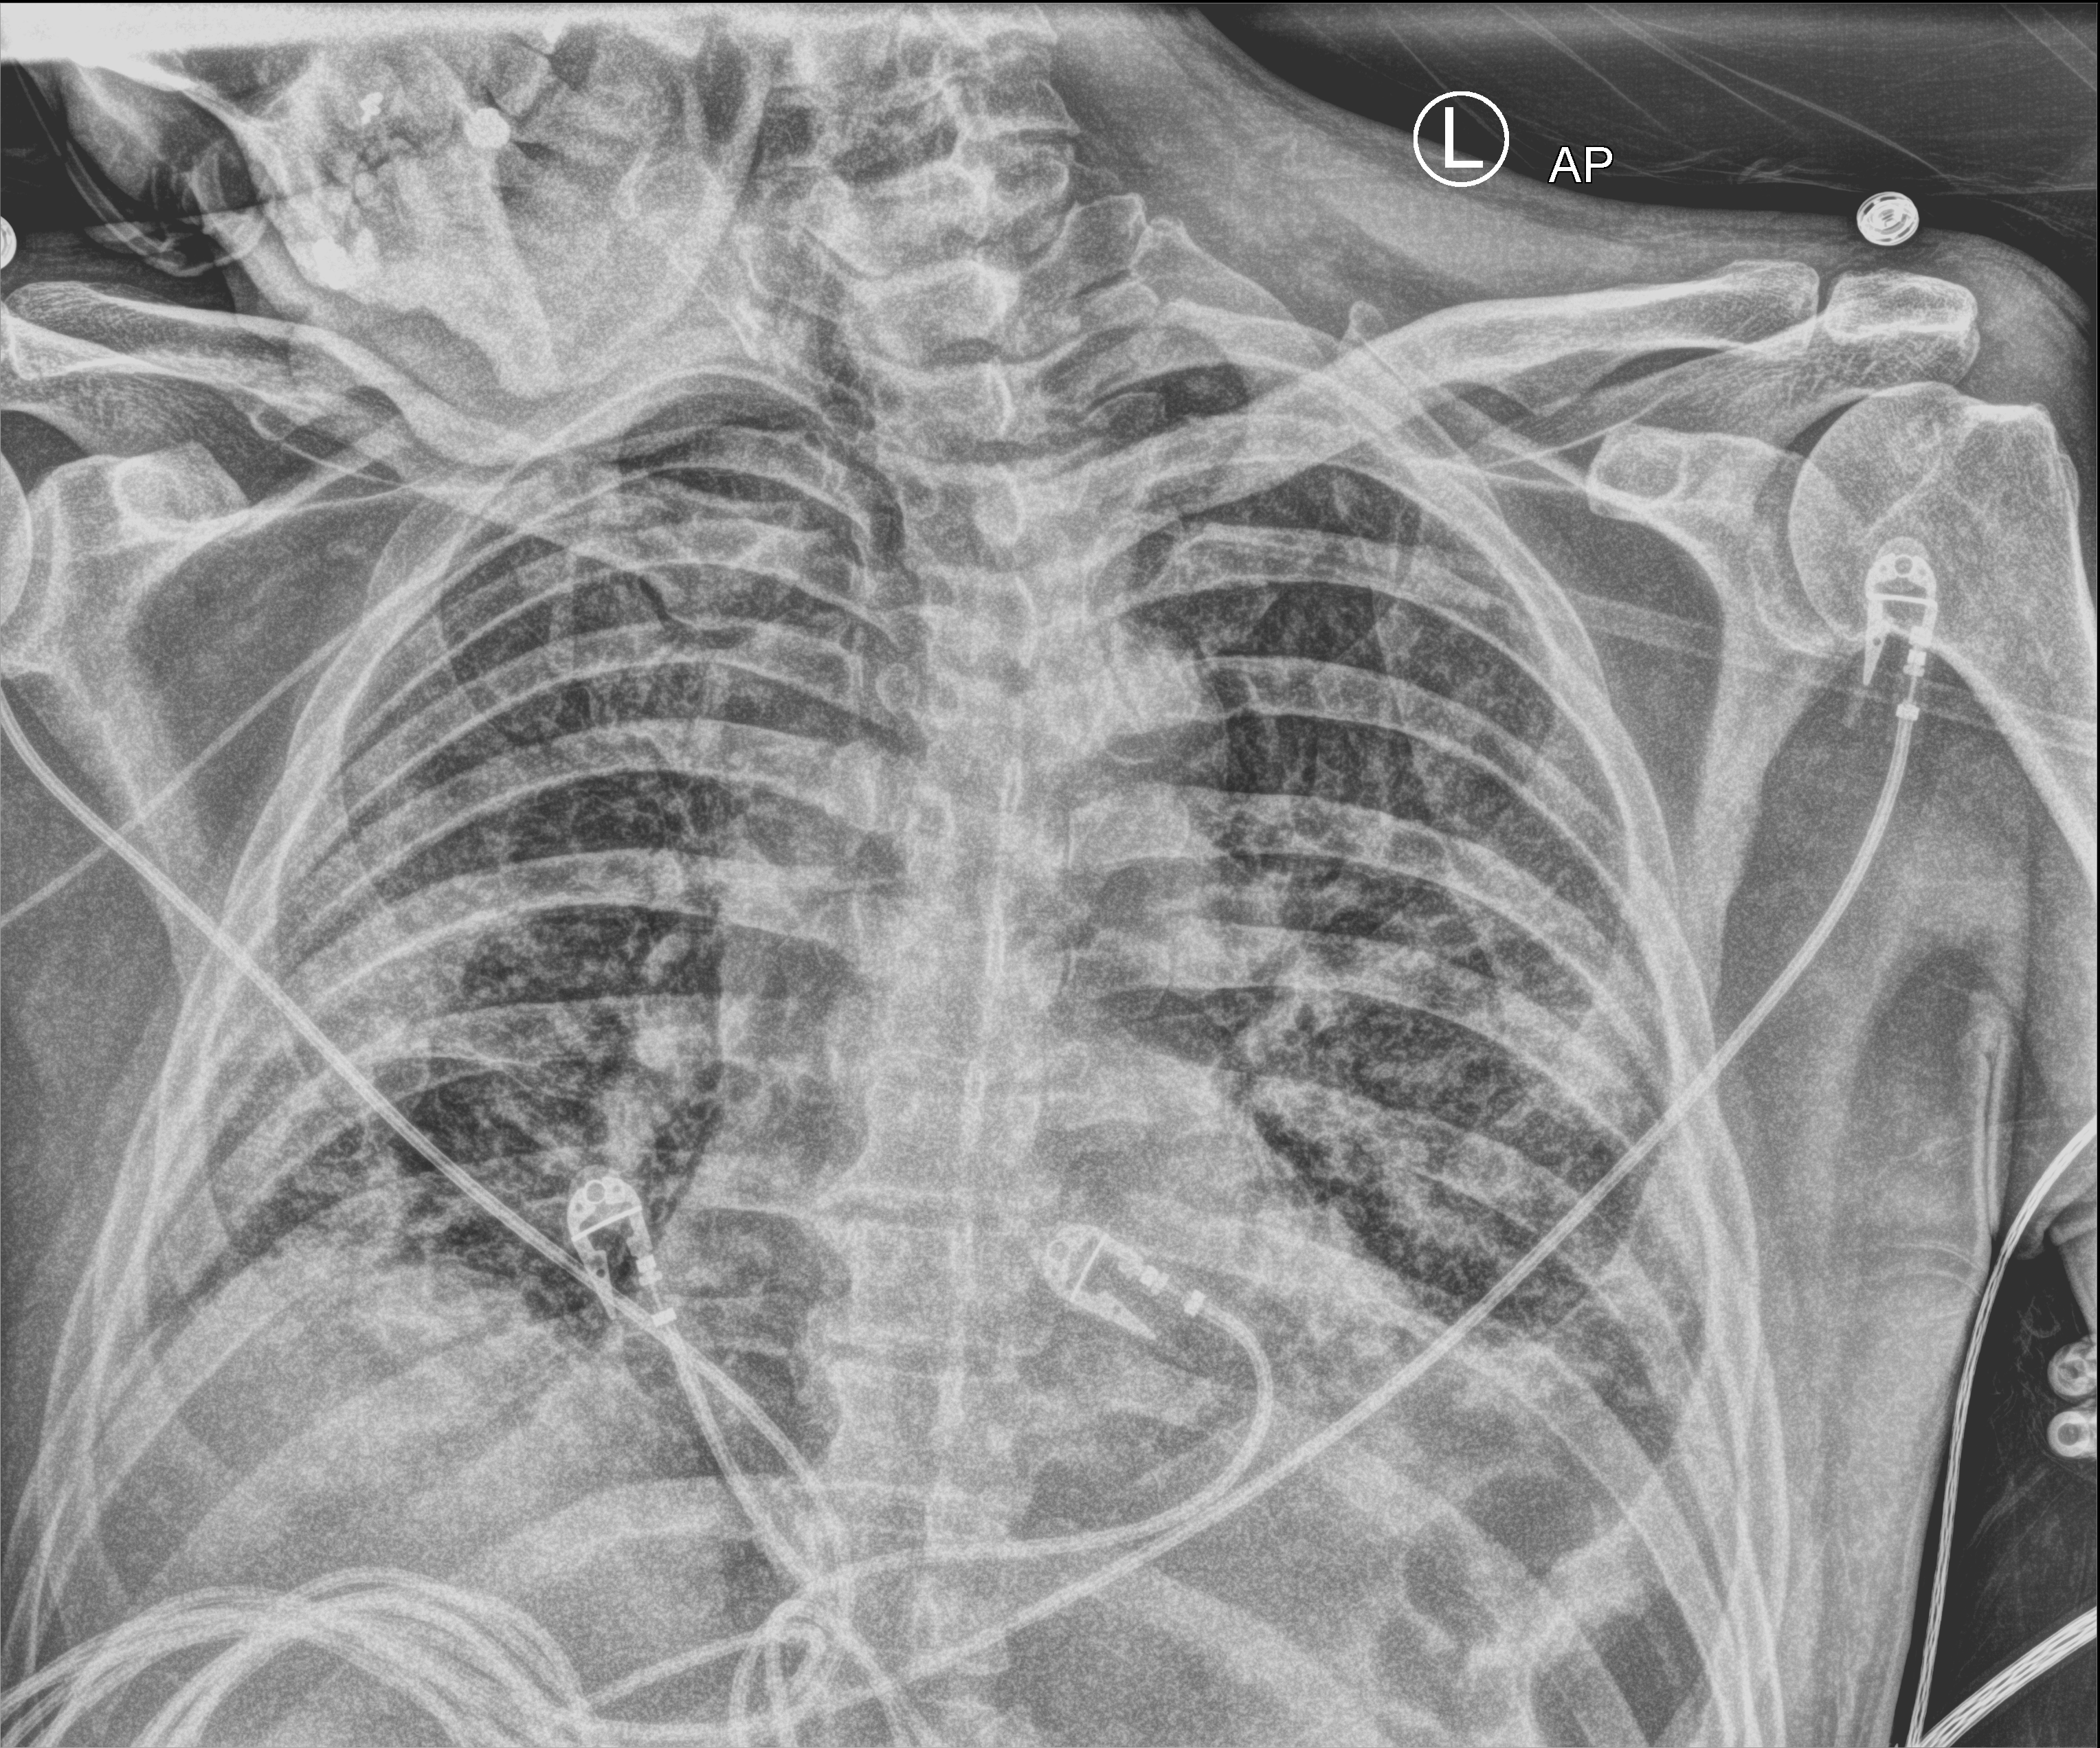
Portable chest radiograph, anteroposterior (AP) projection. Patient hospitalised with COVID-19; male, aged 60–74 years.
Admission-level facts for this patient (not findings on this image; timing relative to this image not recorded): hypertension (admission record): no; length of hospital stay: 26 days; COPD (admission record): no.